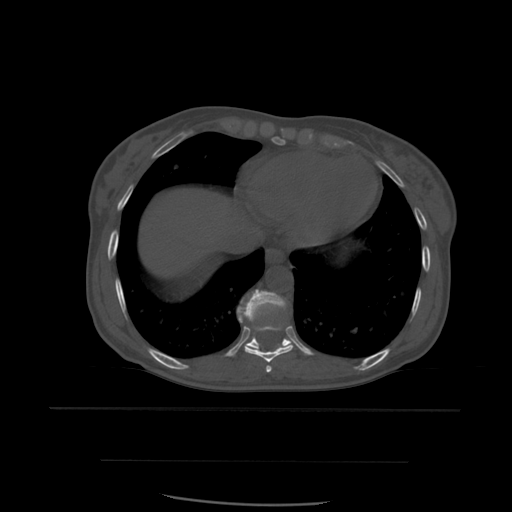
CT including the spine, one axial slice. Position 329 of 574 along the scan axis. Bone window (W 1800 / L 400 HU). 1.25 mm slice thickness. 512 × 512 image matrix. Patient age 48 years. From the clinical record (not read from this slice): primary cancer: lung; vertebrae with lytic lesions (as recorded): T11.
Structures marked on this image (semi-automatically segmented with operator editing):
- T10 vertebra: box from (x=237, y=290) to (x=291, y=349) px
- T8 vertebra: (x=266, y=366)–(x=272, y=373)
- T9 vertebra: (x=239, y=315)–(x=294, y=363)